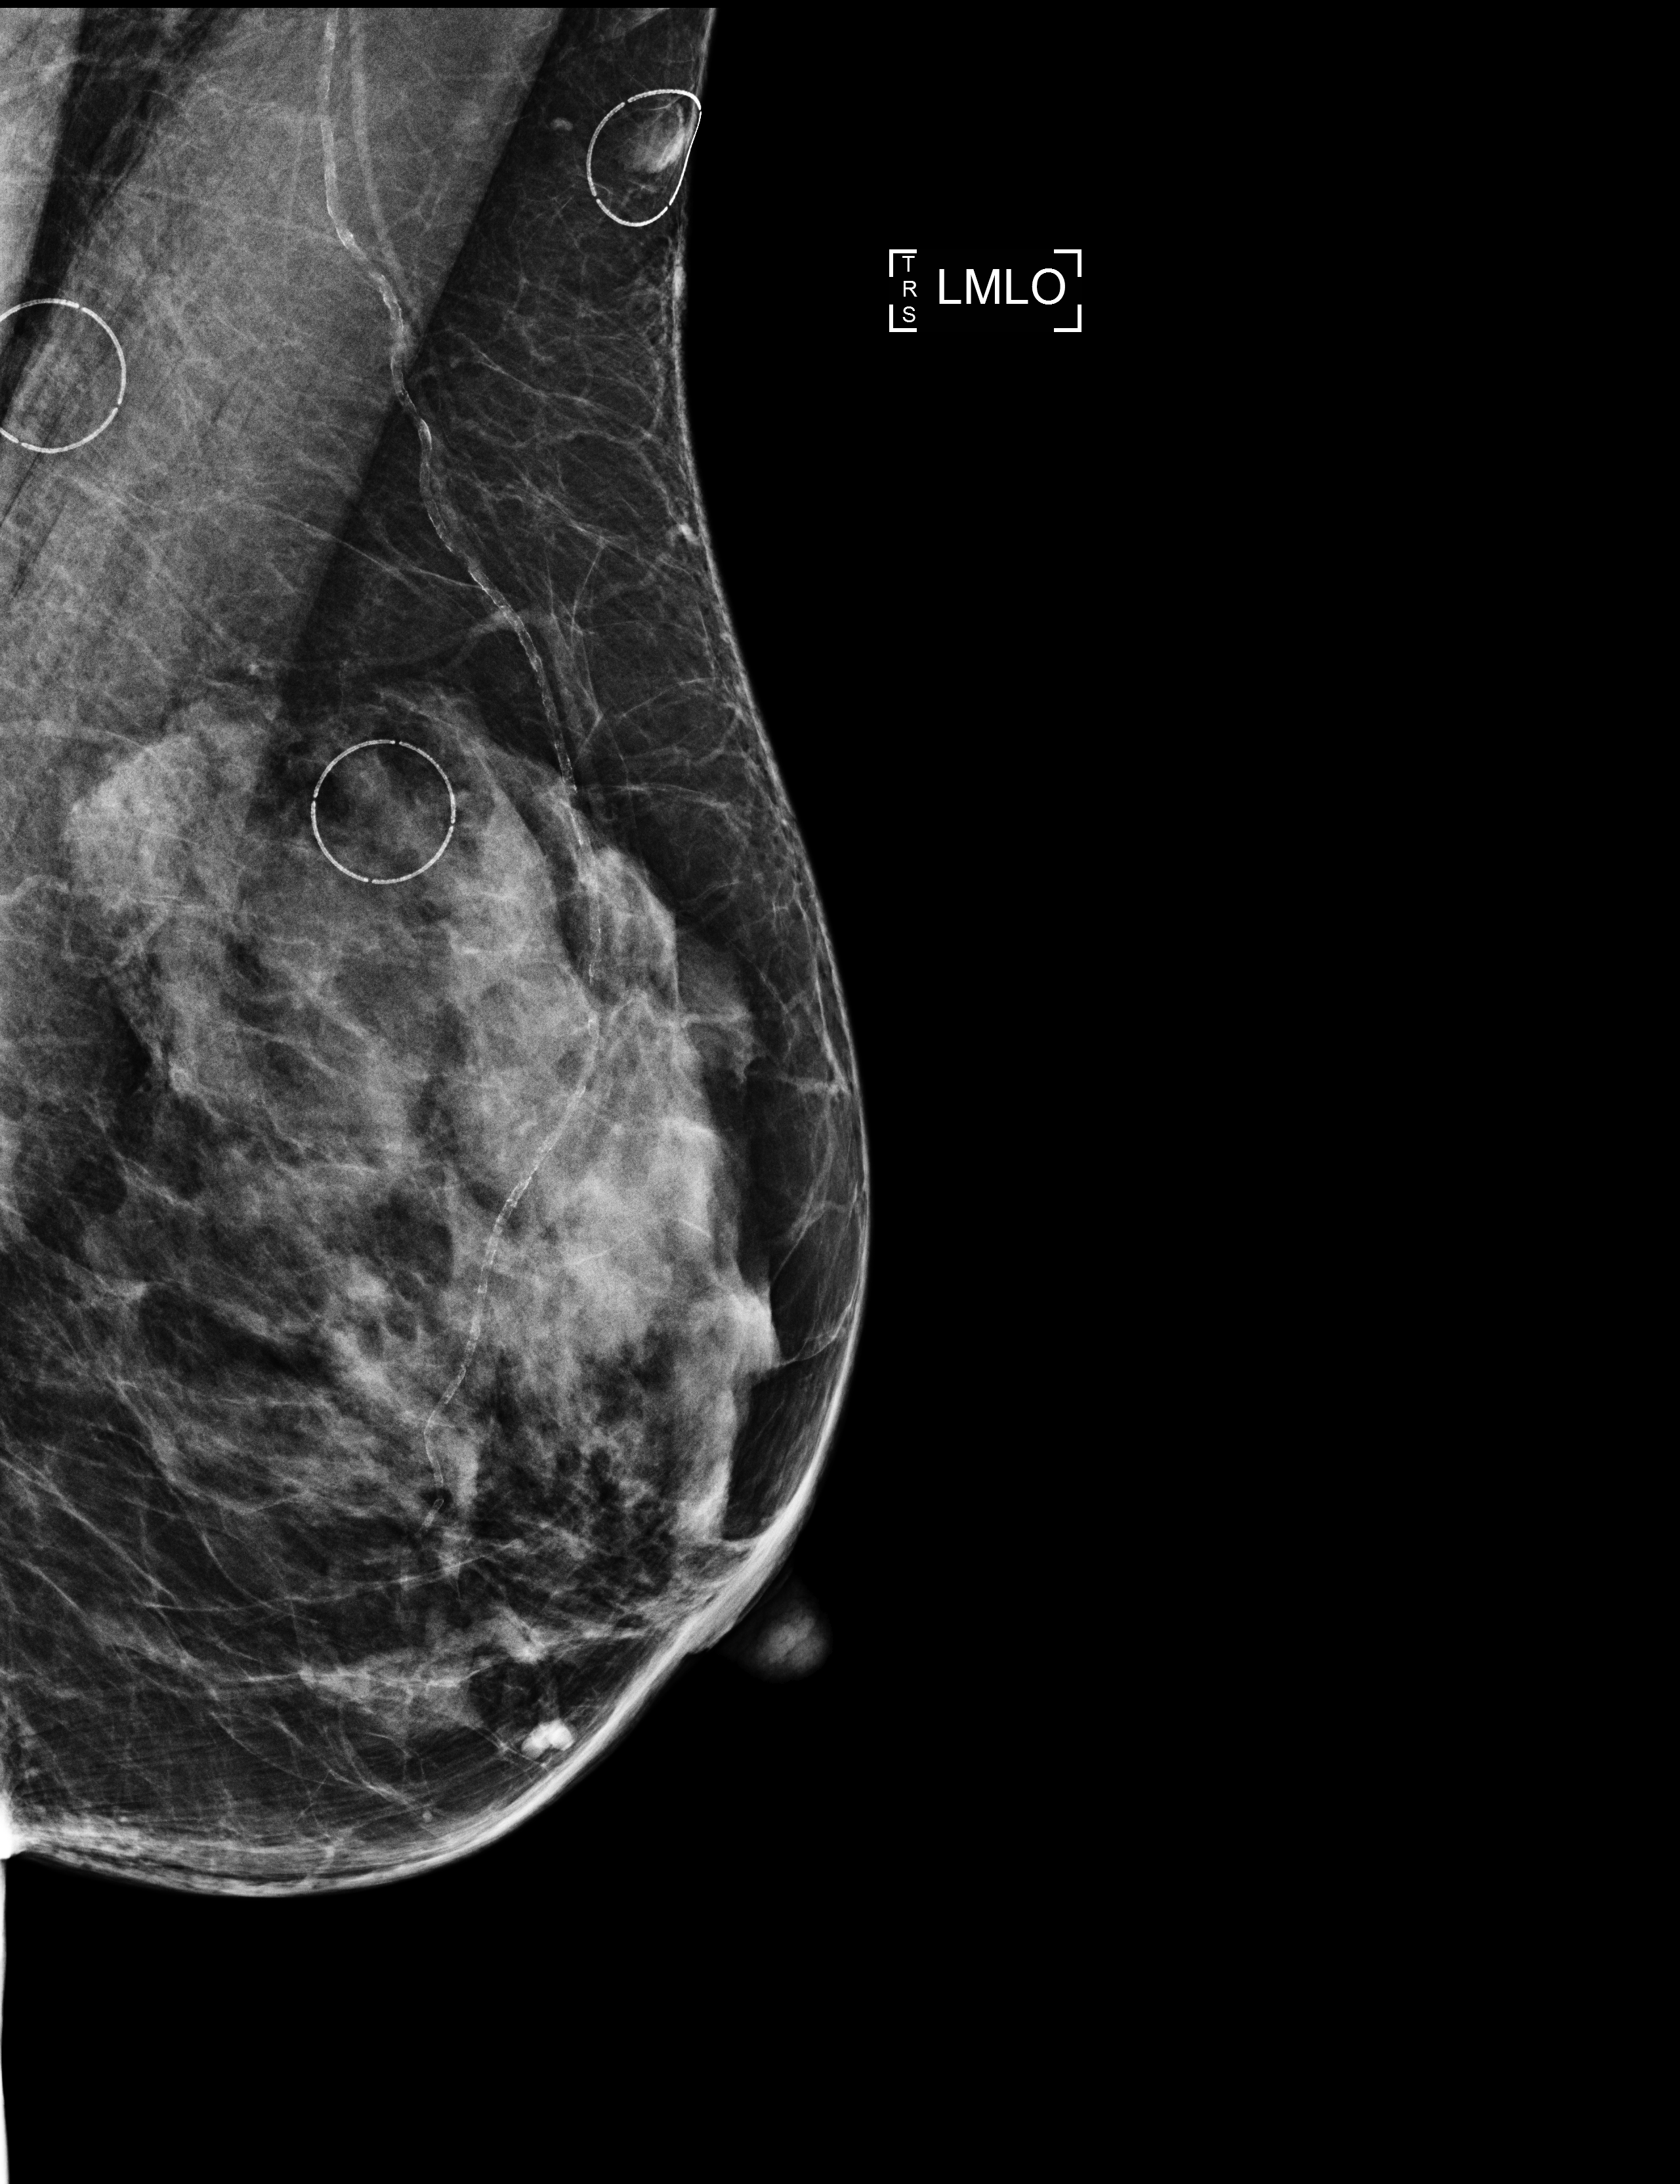
Digital mammogram (FFDM); left breast; MLO view; annual screening mammography examination; compressed breast thickness 40 mm. Patient: female, 75 years.
BI-RADS breast density category at the screening exam (both breasts, scale 1–4): 3.